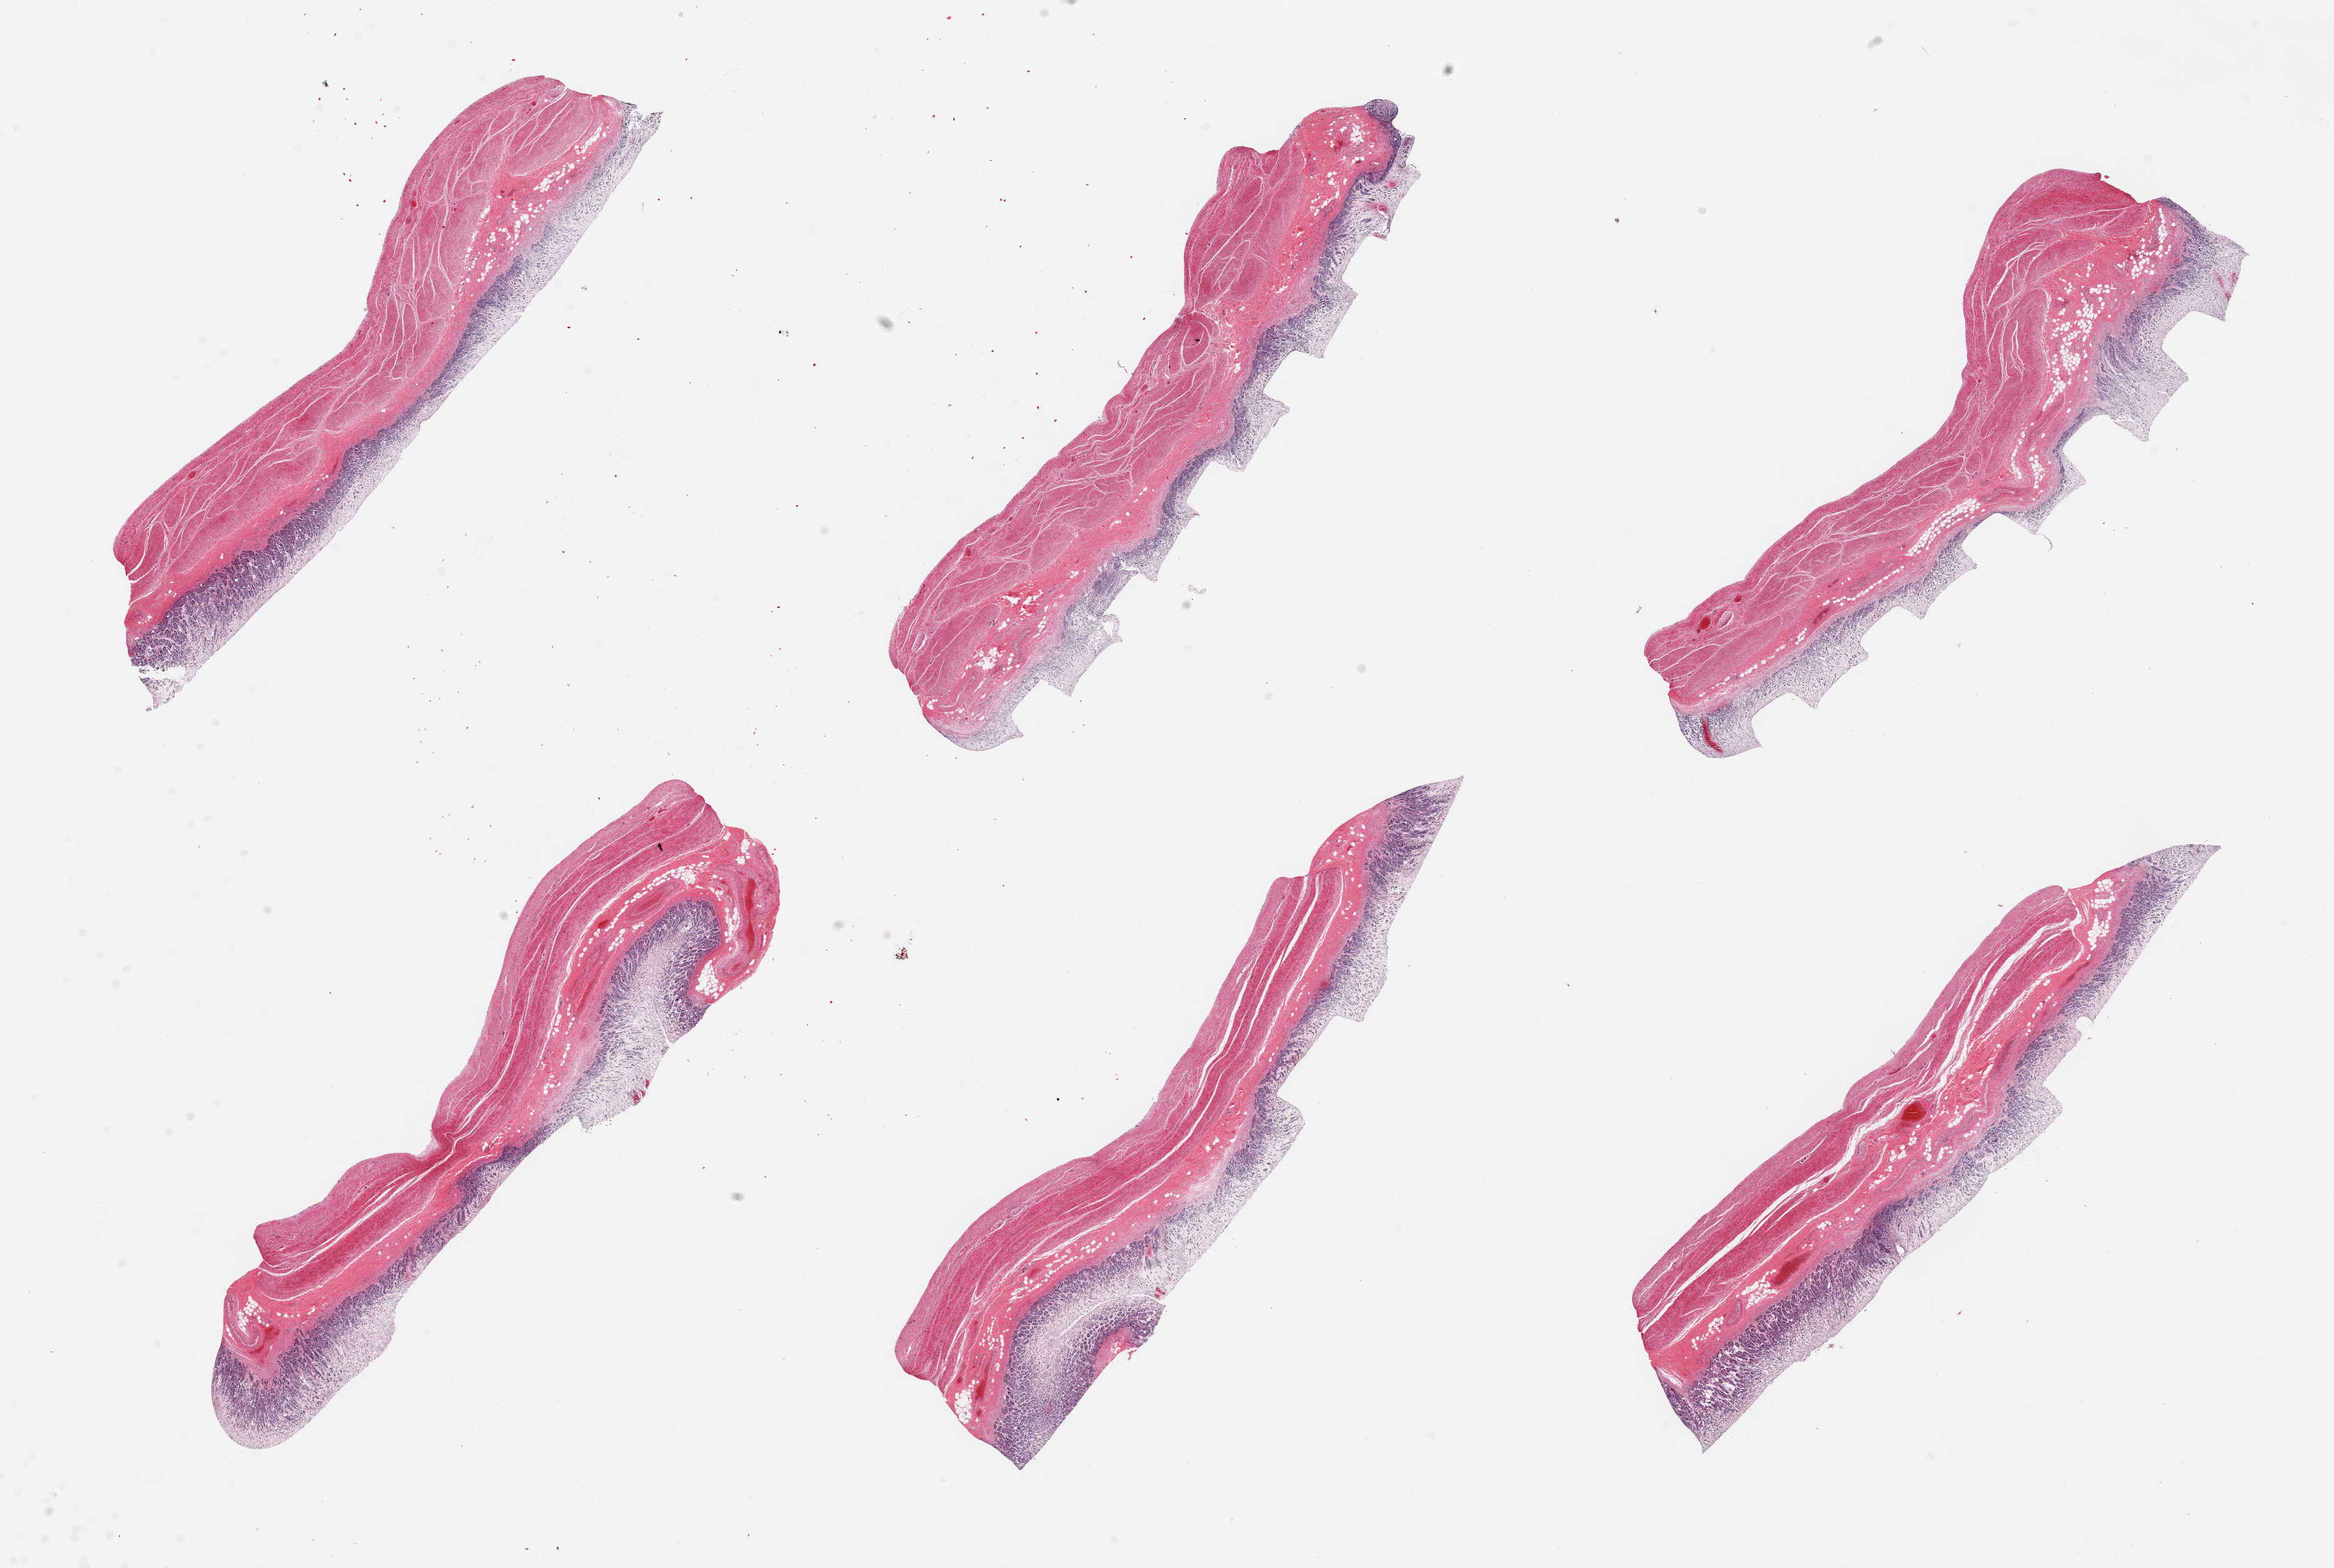
Hematoxylin and eosin (H&E) whole-slide image — a low-resolution overview of the entire scanned area, about 29.5 x 19.8 mm (slide scanned at 20x), PAXgene-fixed paraffin-embedded (PFPE) section, section of stomach (target tissue), donor tissue sample. Donor: male.
Reviewer comment on this tissue sample: 6 pieces; mucosa = 3; muscularis = 1.